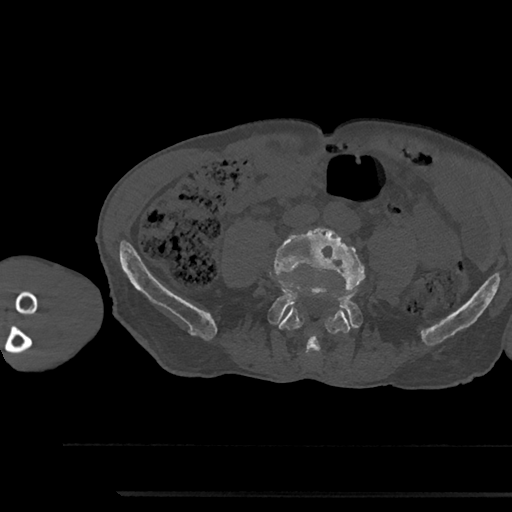
CT including the spine, one axial slice; position 383 of 797 along the scan axis; reconstruction kernel Br40s/3; bone window (W 1800 / L 400 HU); 0.5 mm slice thickness; 512 × 512 image matrix, field of view 367 × 367 mm. Male patient, age 79 years. Case-level facts recorded for this patient, not image findings: primary cancer: prostate.
Structures marked on this image (semi-automatically segmented with operator editing):
- L4 vertebra: bounding box [x1, y1, x2, y2] px = [272, 228, 364, 354]
- L5 vertebra: [269, 294, 362, 328]